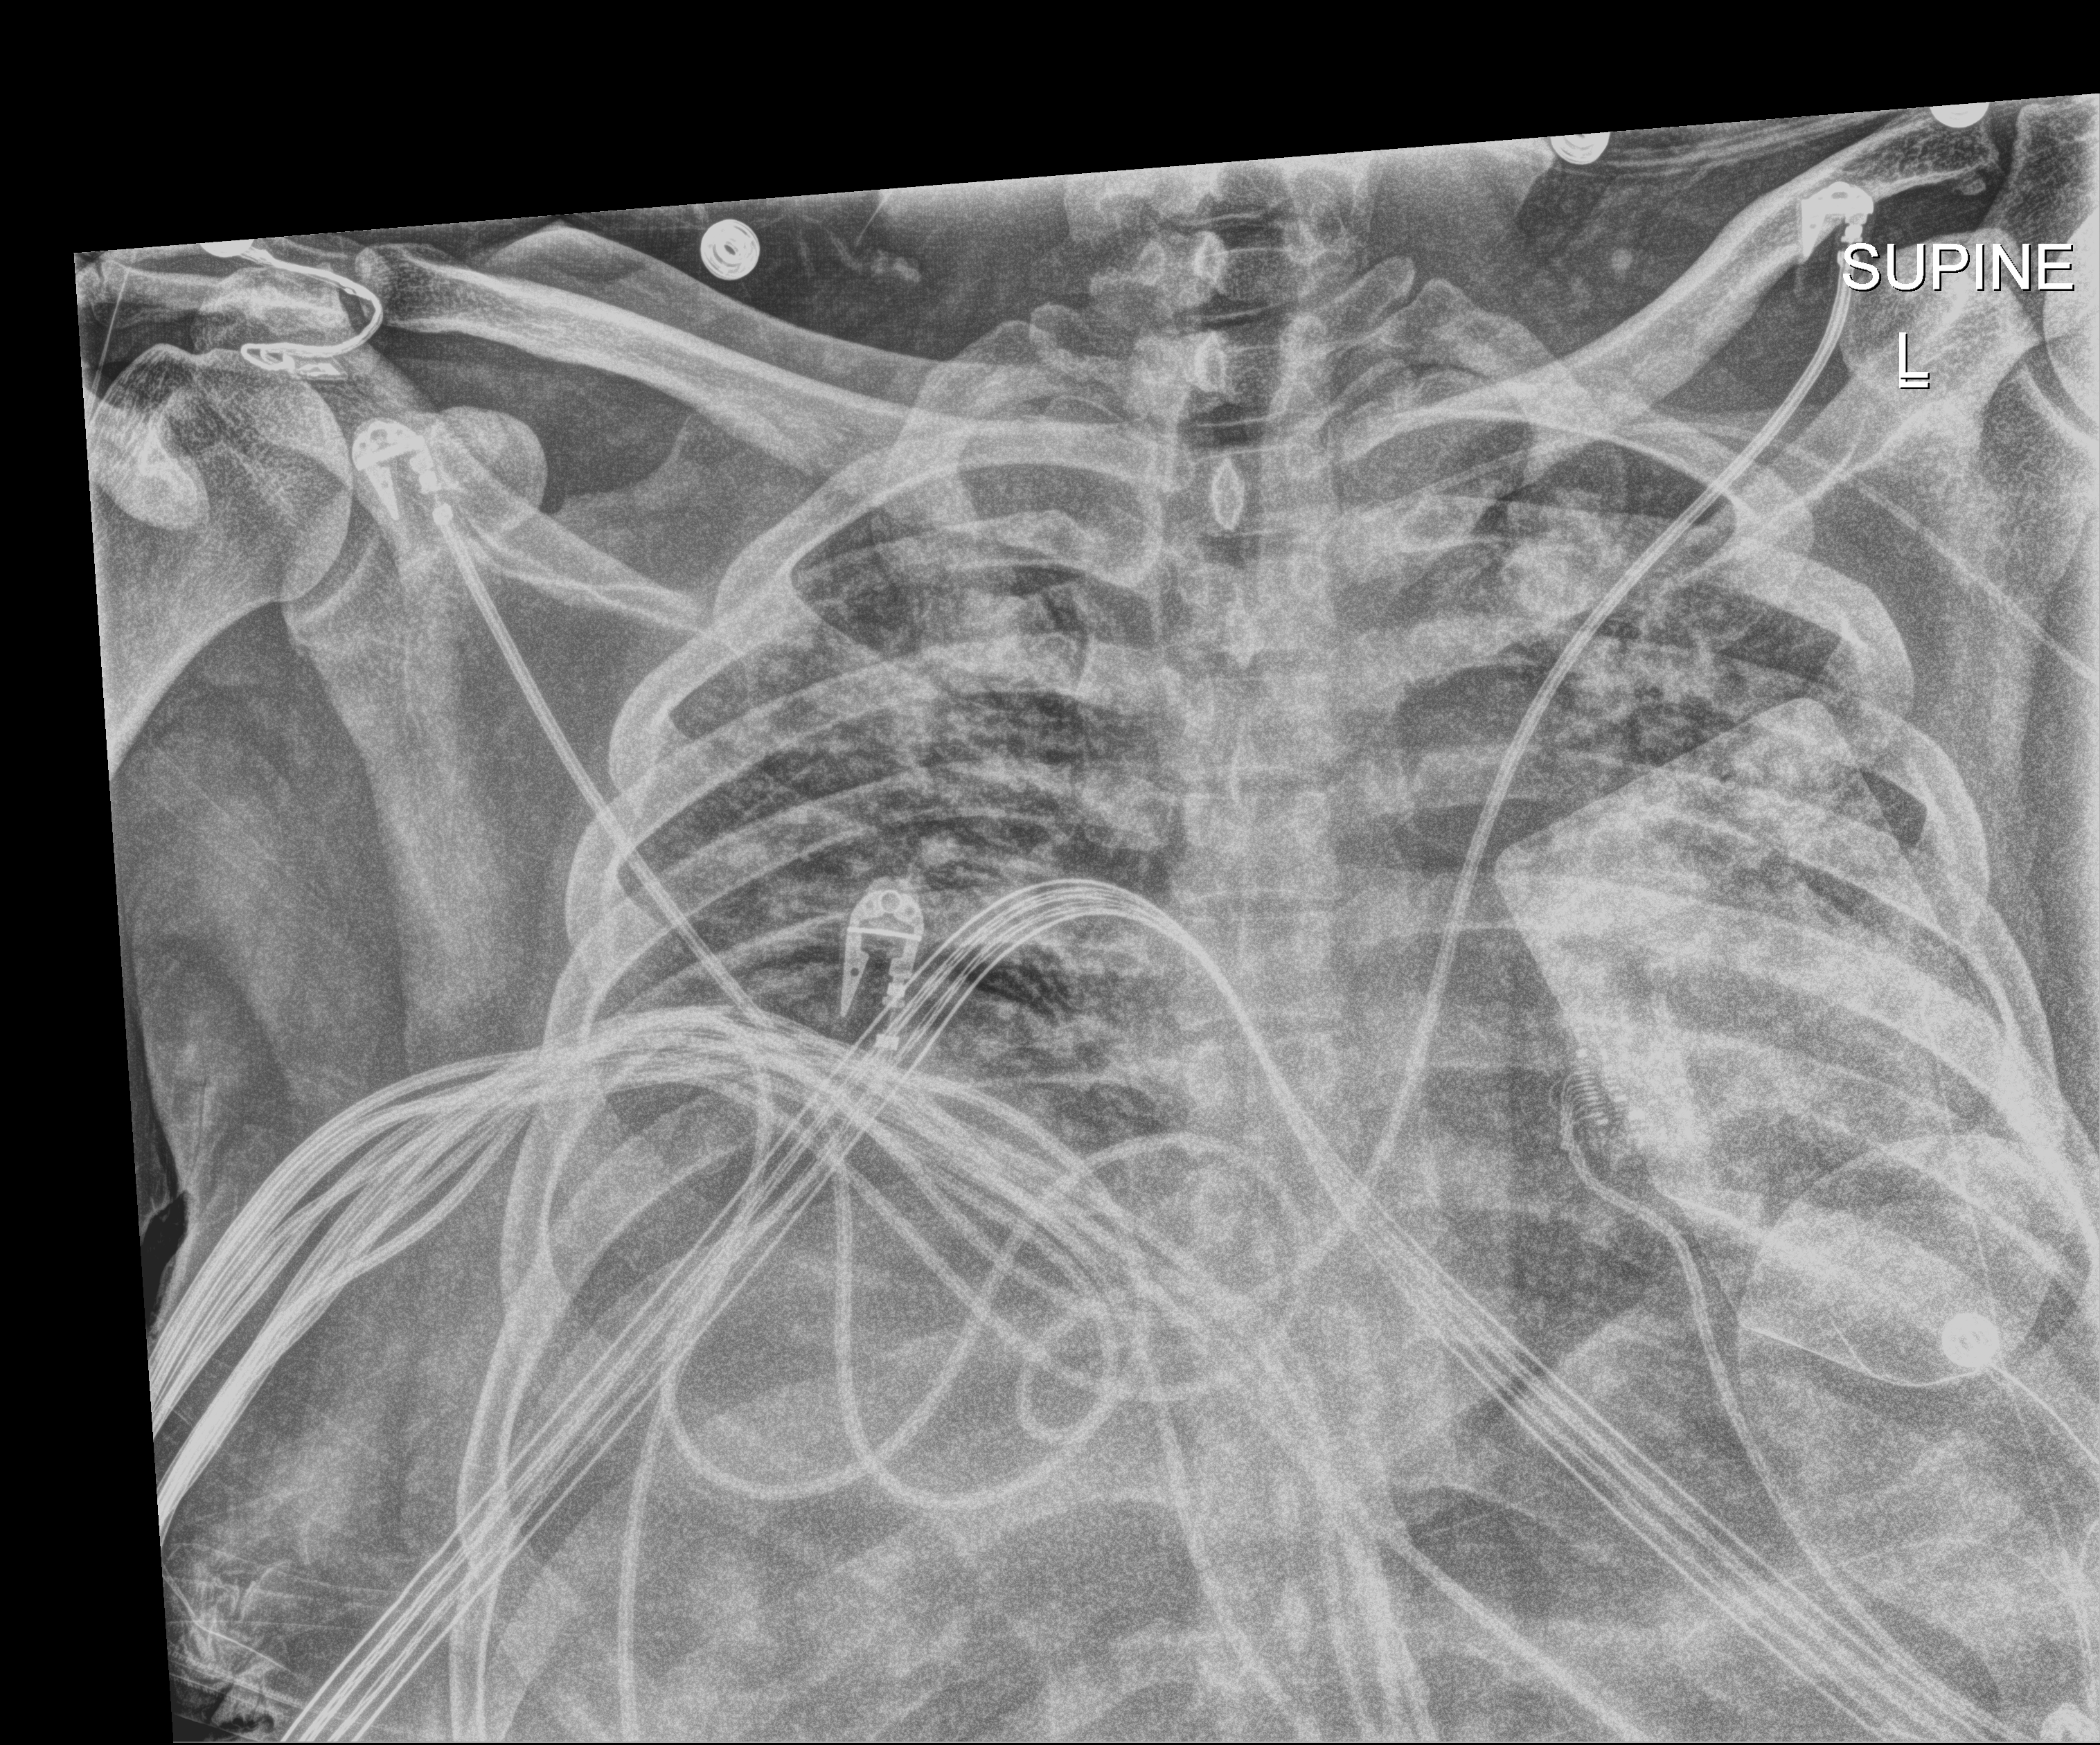
Portable chest radiograph; anteroposterior (AP) projection. Male patient hospitalised with COVID-19, age 18–59 years.
Hospital-stay facts (about this admission, not read from this image; timing relative to this image not recorded):
- admitted to intensive care during this hospital stay: yes
- length of hospital stay: 29 days
- mechanically ventilated during this hospital stay: yes